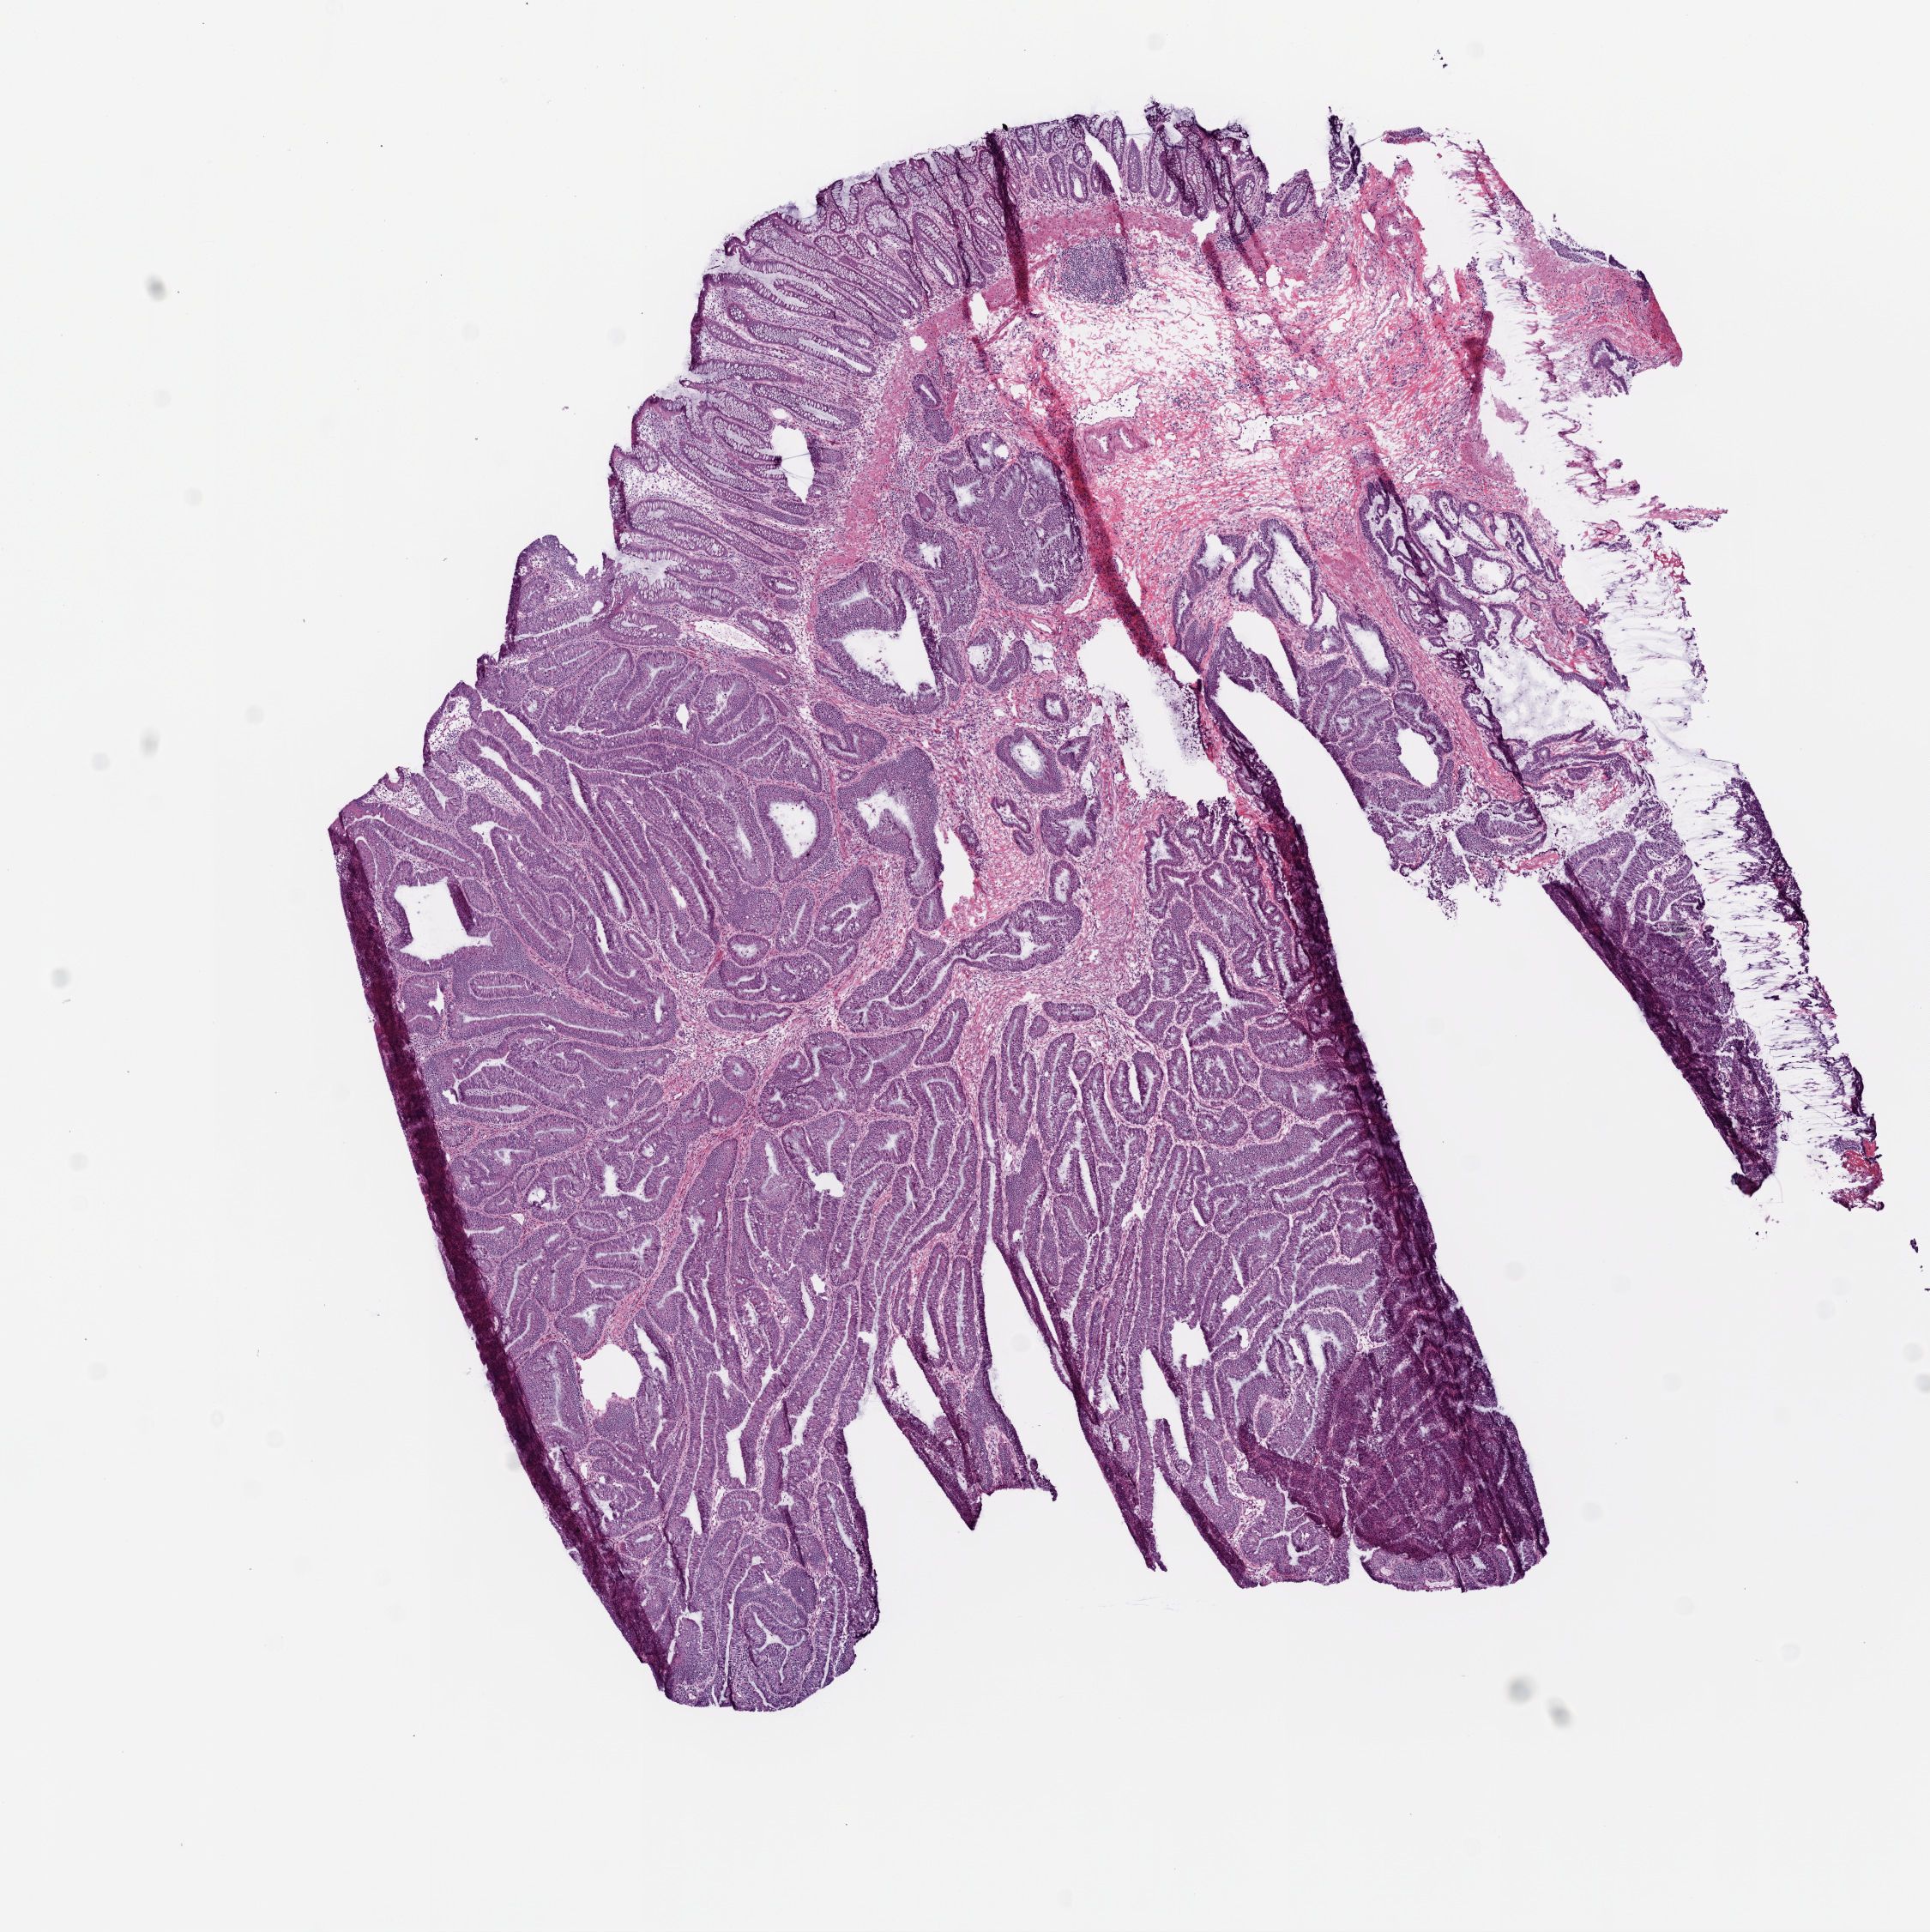
H&E whole-slide image — a low-resolution overview of the entire scanned area, about 9.0 x 9.0 mm (slide scanned at 20x), frozen section from the top of the tissue portion, sample: primary tumour, rectum. Male, age 72 years at initial diagnosis. Pathologist review of this section (percent, as recorded): tumour cells 60%, tumour nuclei 76%, normal cells 8%, stromal cells 32%, necrosis 0%.
* lymph nodes positive (case pathology): 0 of 19 examined
* histologic diagnosis: Adenocarcinoma, NOS
* AJCC pathologic stage: IIA (6th edition)